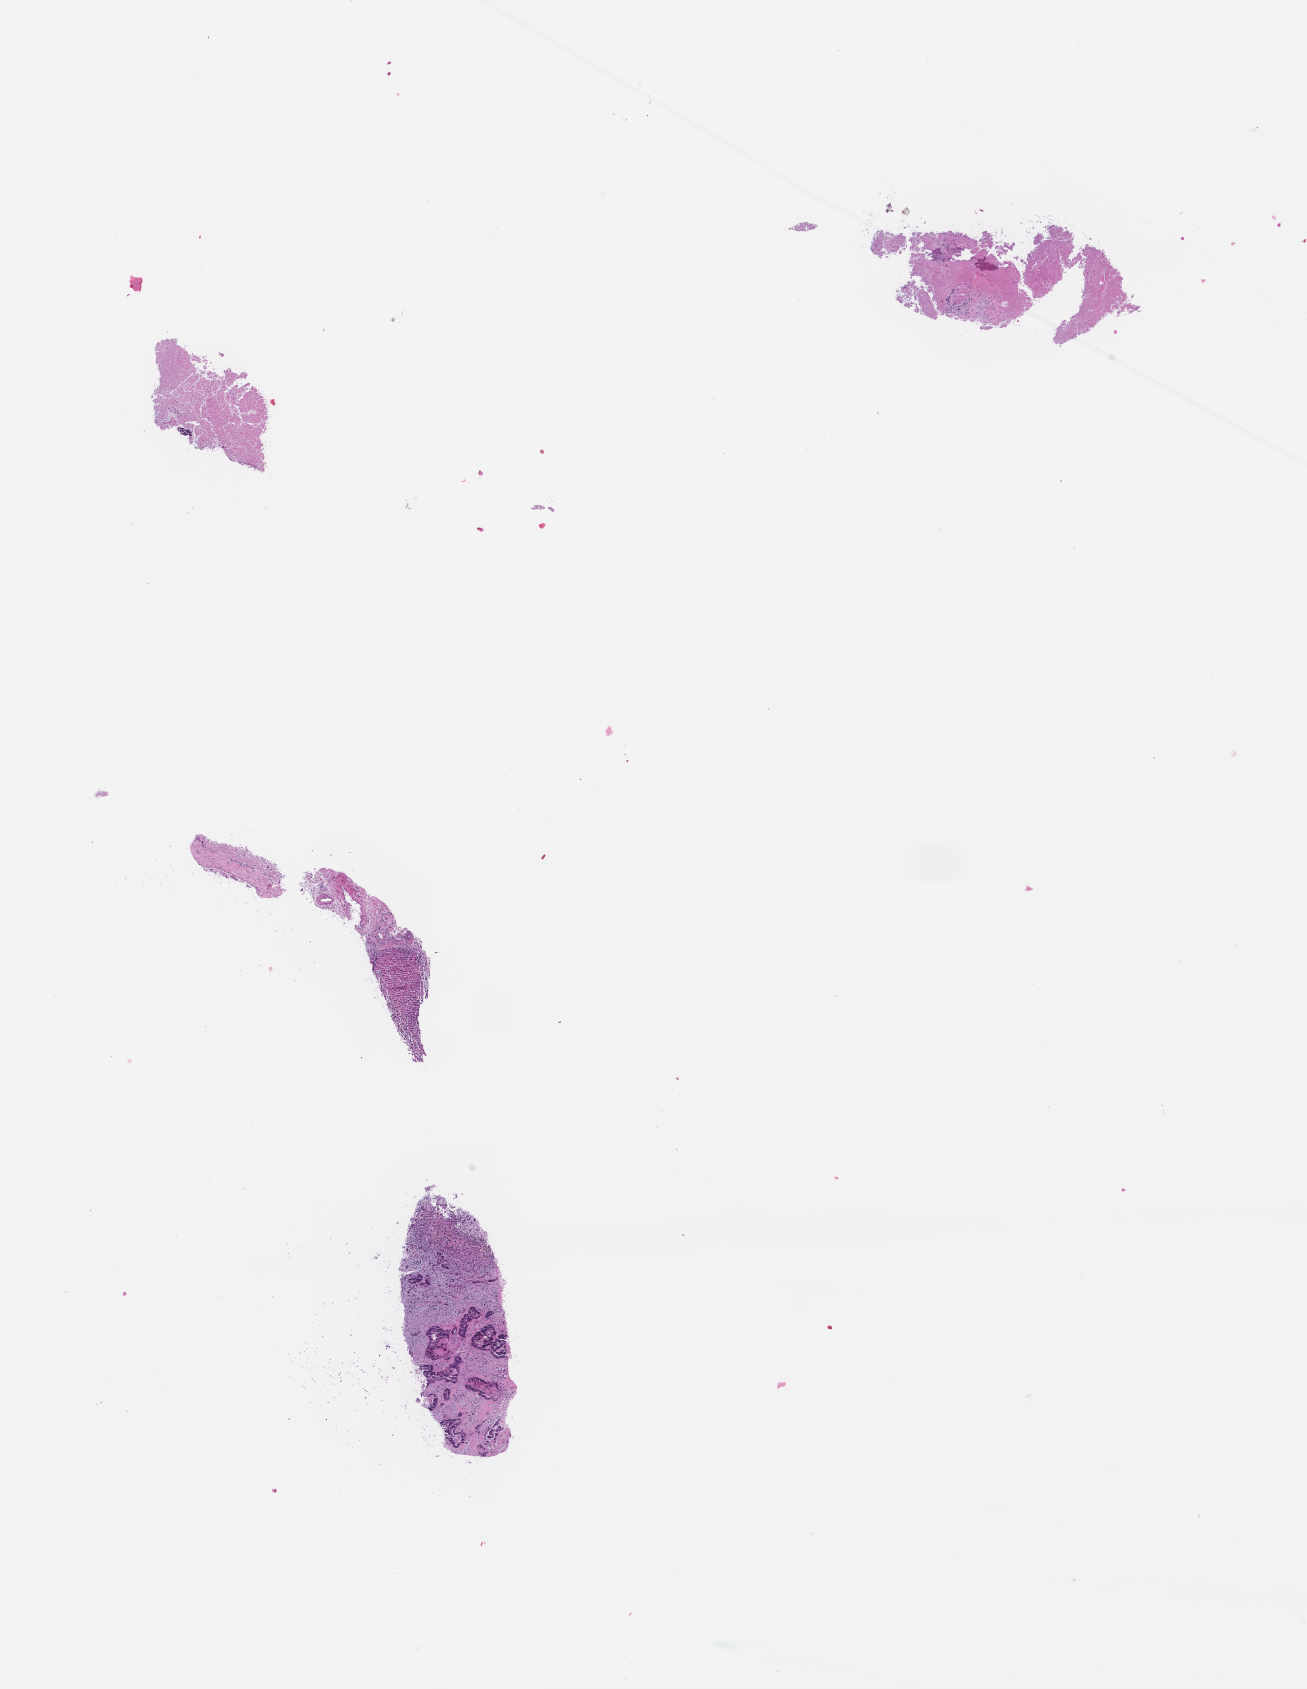
Haematoxylin and eosin whole-slide image, low-resolution overview of the scanned area, about 10.6 x 13.6 mm; formalin-fixed, paraffin-embedded (FFPE) tissue. Female patient.
This section: metastasis (sampled organ not recorded). Primary diagnosis of the patient: Colorectal Carcinoma.